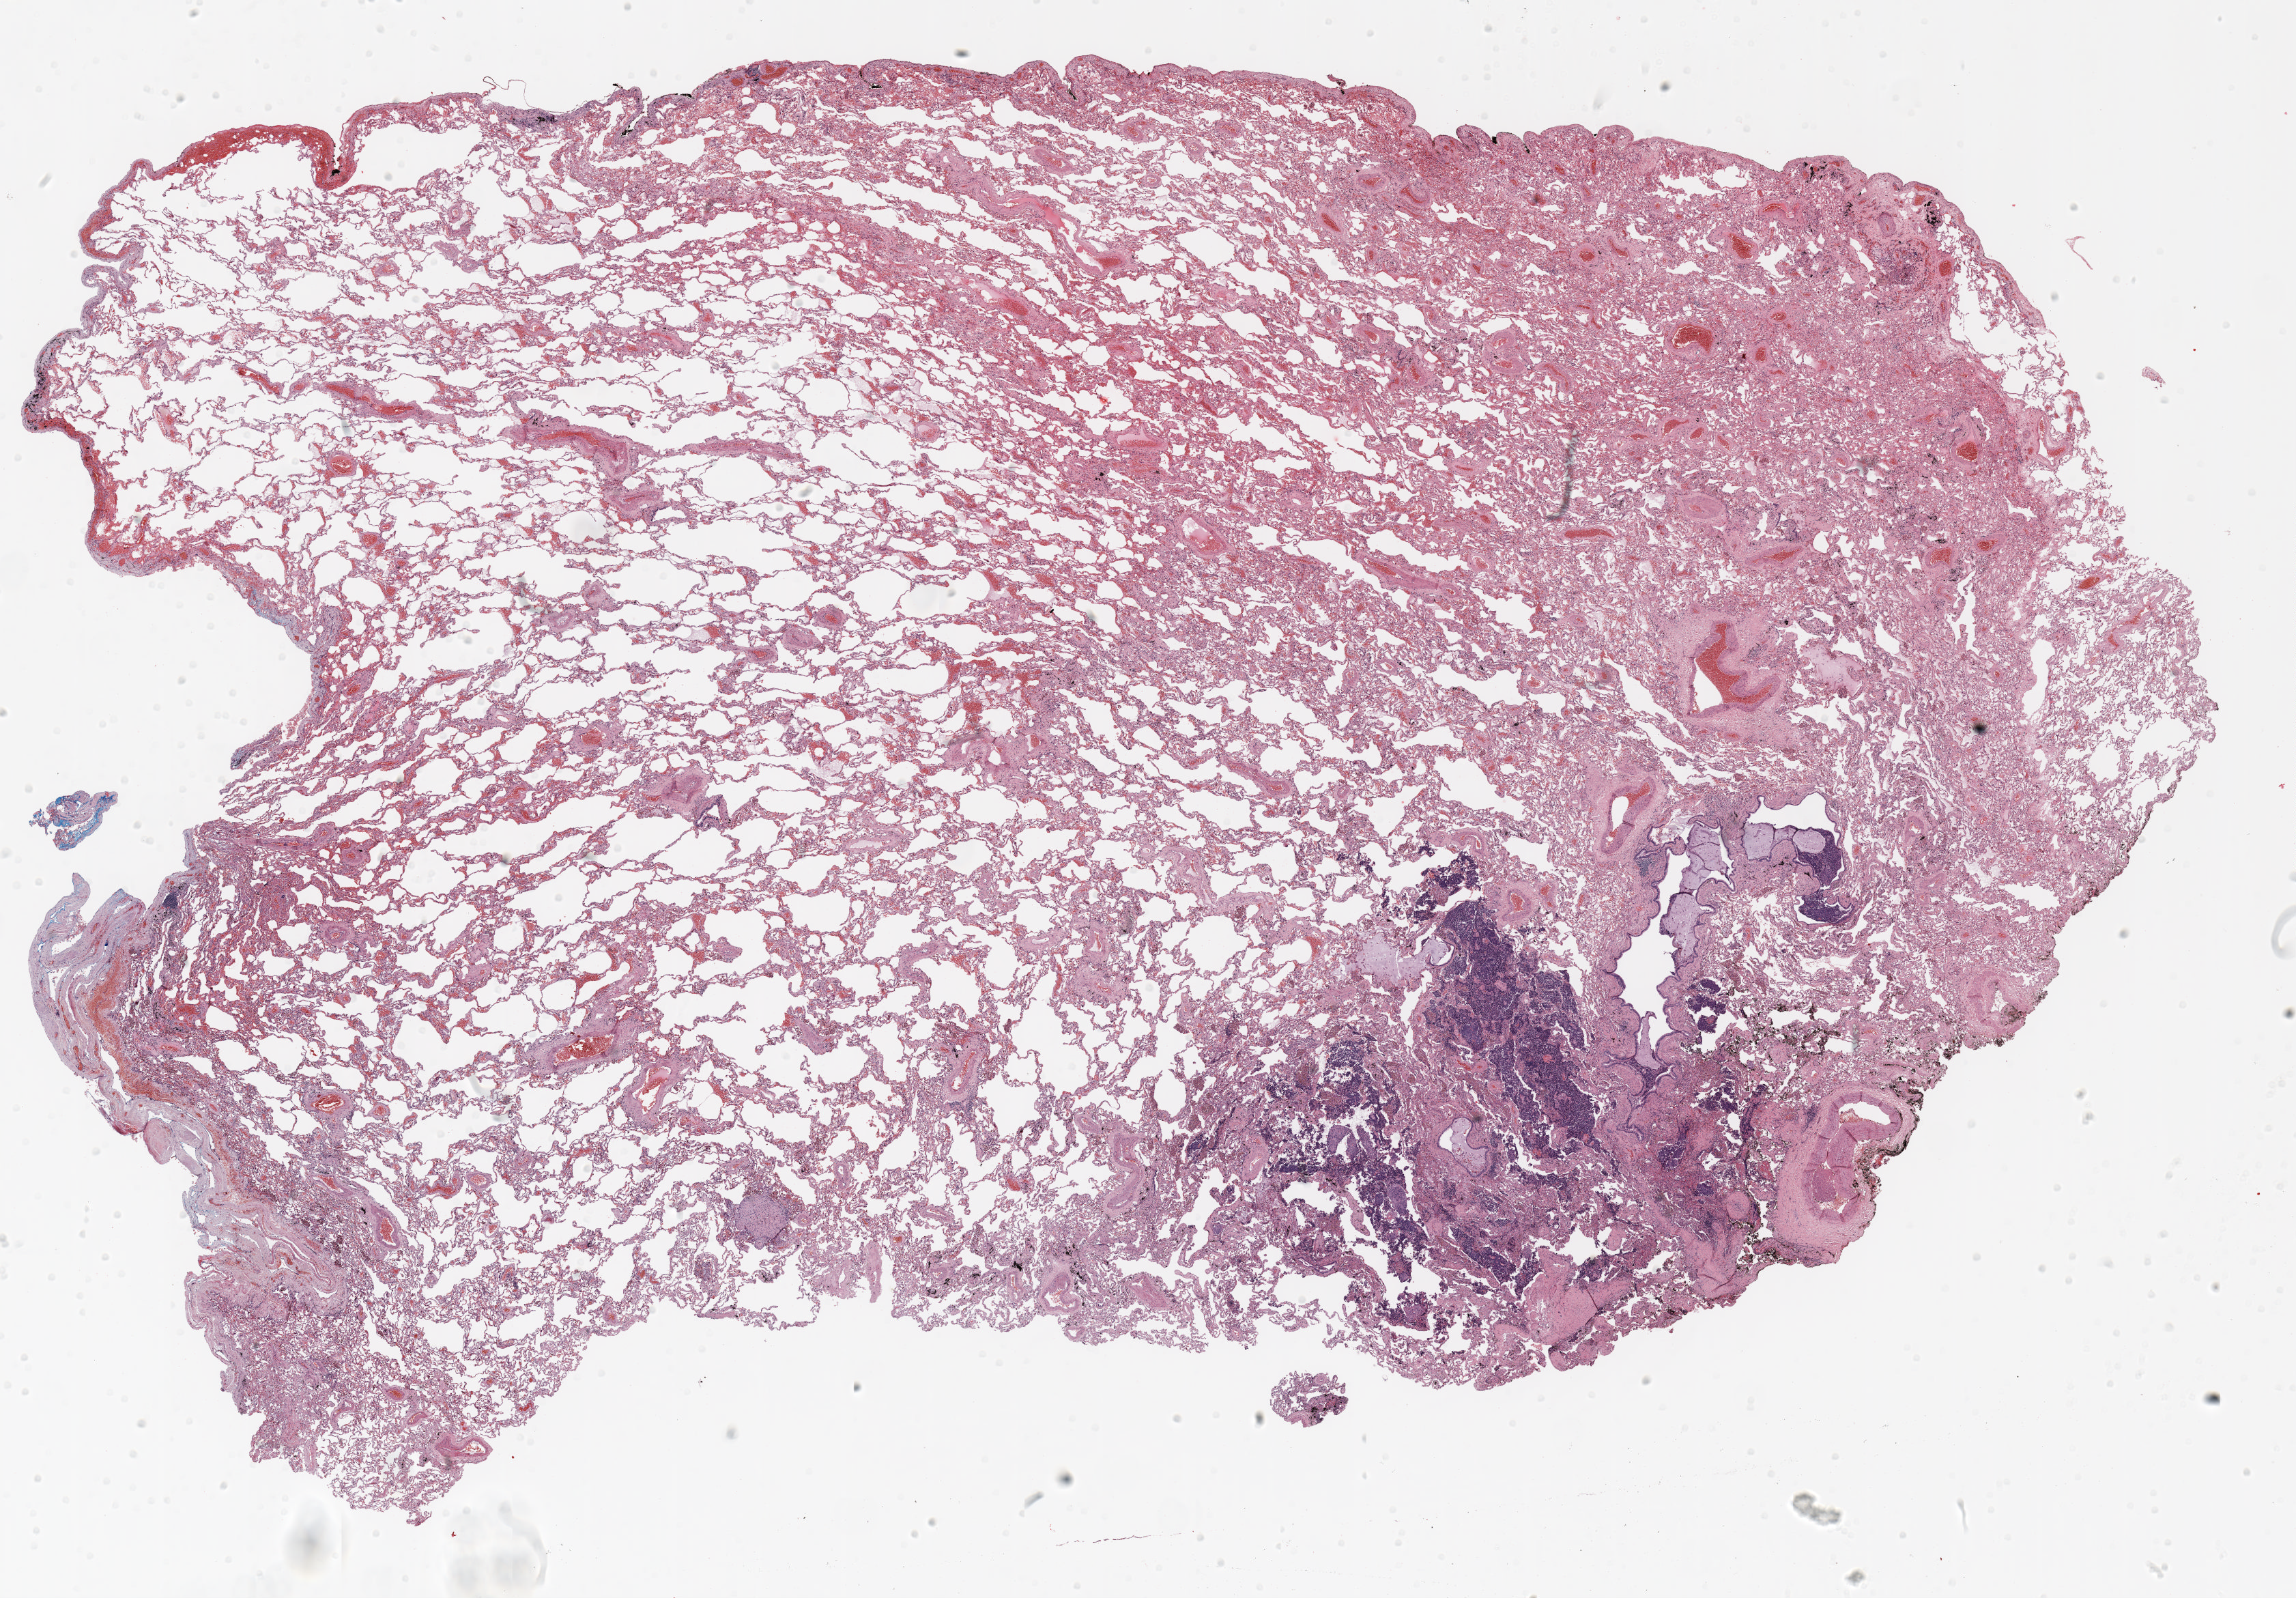
H&E-stained whole-slide image, shown as a low-resolution overview of the whole scanned area (about 27.0 x 18.8 mm), FFPE section, lung. Male patient, aged 65 at enrolment. Current smoker at enrolment. Grade: poorly differentiated (G3).
Stage (AJCC 6th edition): IA. Primary tumour location (clinical record): left upper lobe. Participant's lung-cancer diagnosis: Squamous cell carcinoma, NOS (ICD-O-3 8070/3). Tumour size (pathology): 18 mm.